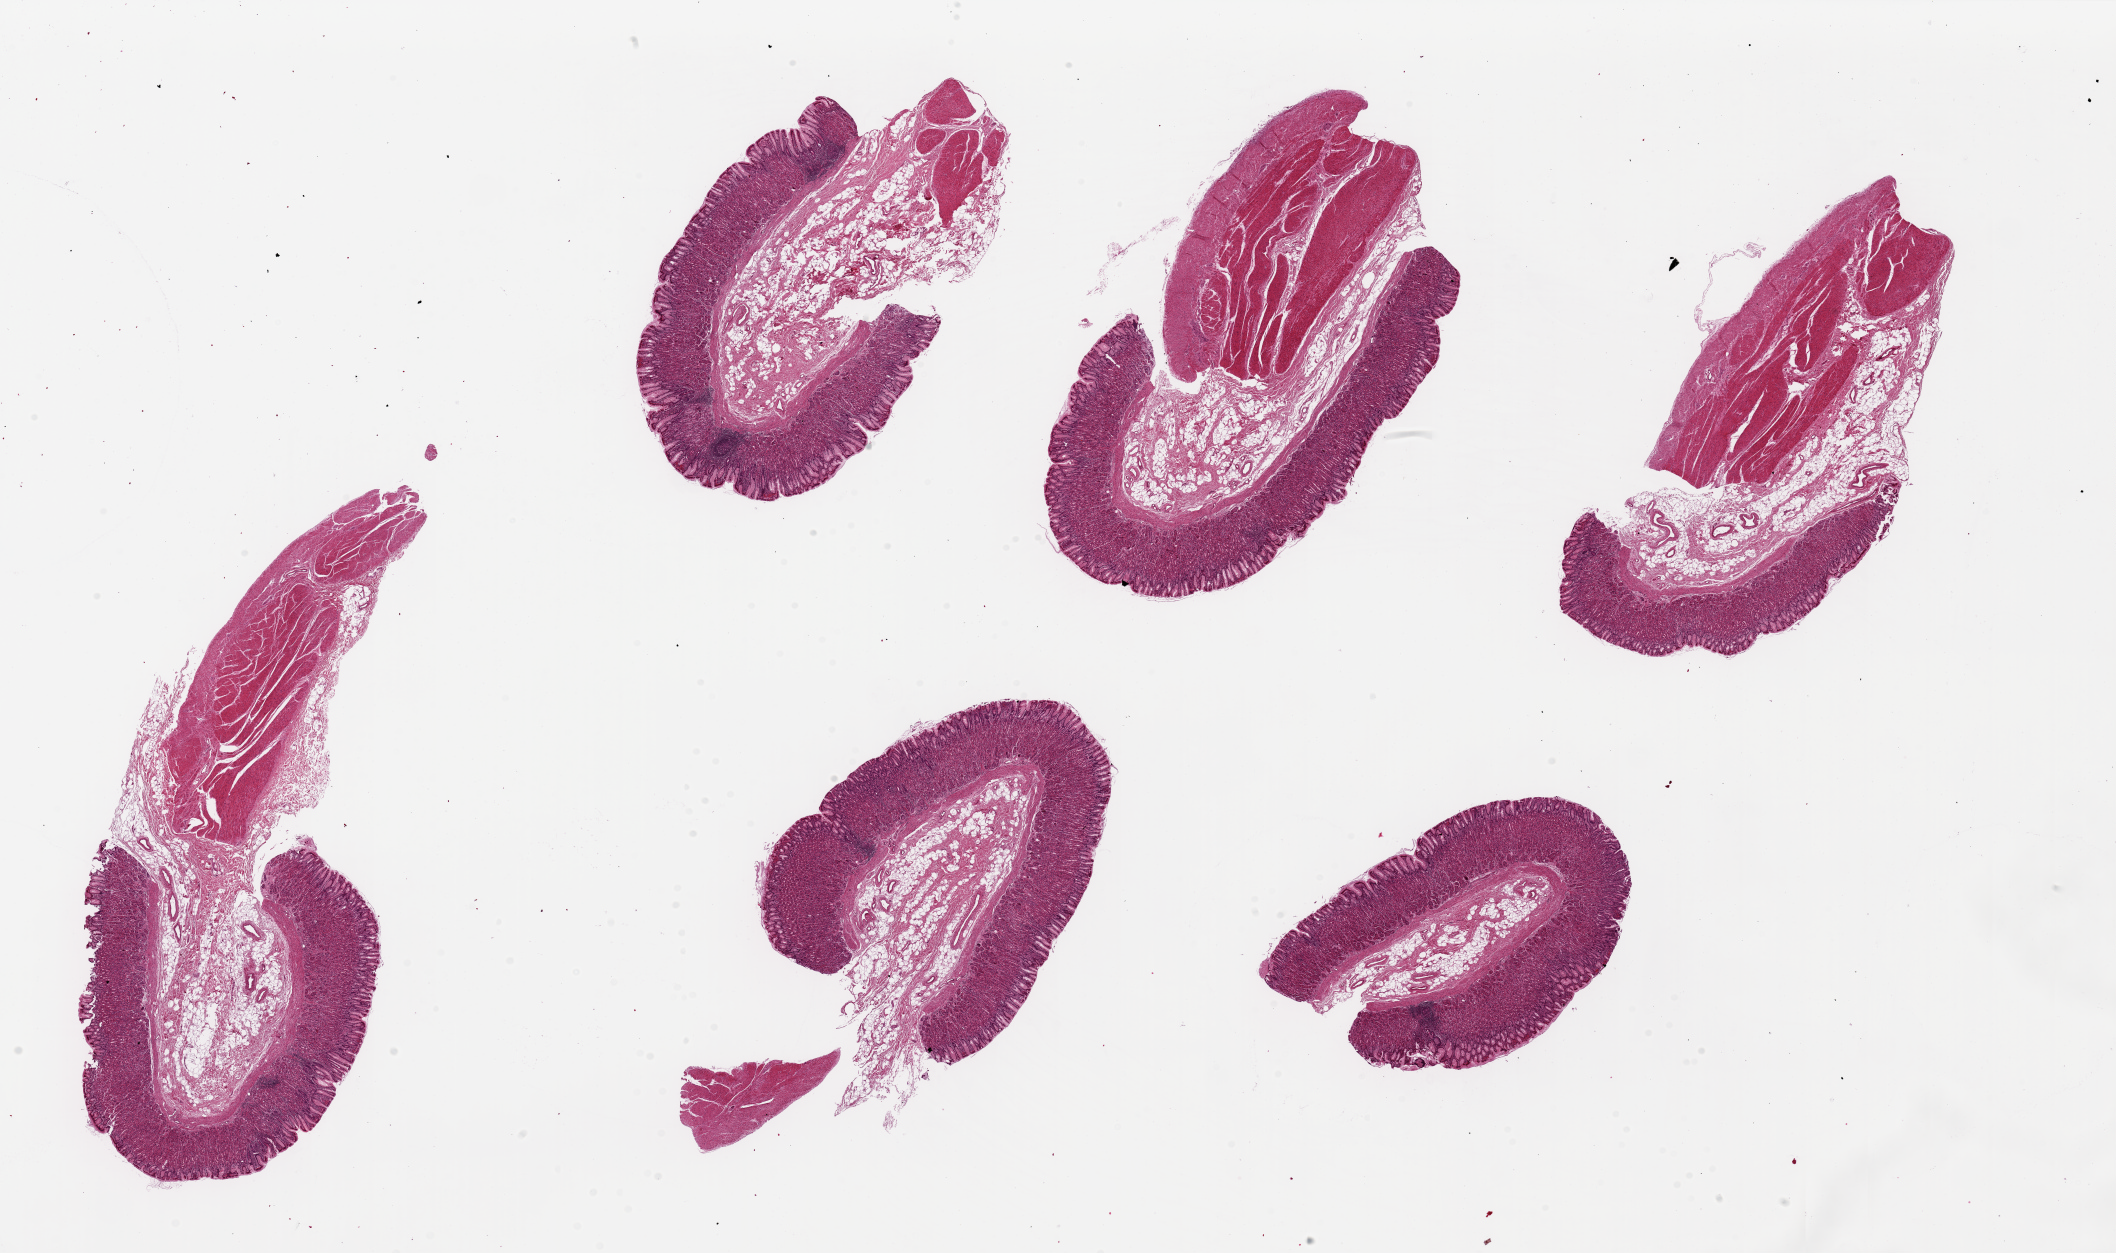
Haematoxylin and eosin whole-slide image, whole scanned area (about 33.5 x 19.8 mm, from a 20x scan) shown as a low-resolution overview. PAXgene-fixed paraffin-embedded (PFPE) section. Section of transverse colon (target tissue). Tissue donor sample. Donor sex: male.
- reviewer comment on this tissue sample: 6 pieces, up to 12x5mm; ~10-20% thickness is mucosa, reasonably well preserved